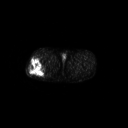
FDG PET of an extremity soft-tissue mass (from a PET/CT study), one axial slice; slice 255 of 267 in the series (ordered by position); 3.27 mm slice thickness; 128 × 128 image matrix. Male patient, age 43 years. Case-level facts recorded for this patient, not image findings: histological type: poorly differentiated synovial sarcoma; grade: high; site of the primary tumour: right buttock.
Annotated regions visible in this slice (expert contour drawn on MRI and transferred to this co-registered scan by the dataset authors):
- gross tumour volume including surrounding oedema: bounding box <28,57,47,77> (left, top, right, bottom; pixels)
- gross tumour volume (mass): <28,57,47,77>